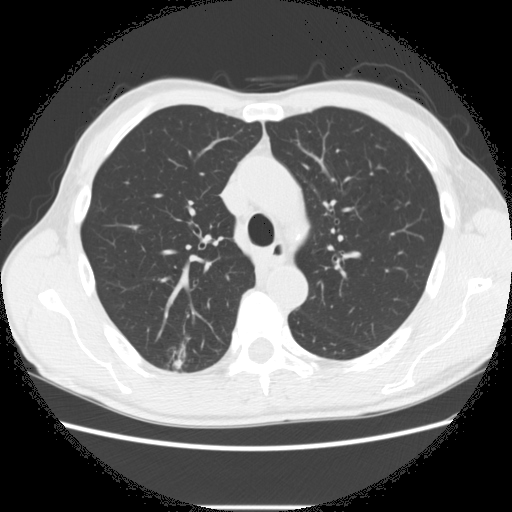
Low-dose screening chest CT, axial slice; second annual screen; lung window (W 1500 / L -600 HU); 2.5 mm slice thickness; standard (soft-tissue) reconstruction kernel (STANDARD); 120 kVp; slice 85 of 282 in the series. Male participant, aged 66 years at enrolment. Former smoker at enrolment.
Lesion marked by an expert reader, bounding box (x1, y1, x2, y2) in pixels: (164, 342, 220, 383). The screening reader recorded 5 non-calcified nodules or masses ≥4 mm on this exam; which of them this box marks is not recorded. Official screen result: positive, change unspecified: nodule(s) >= 4 mm or enlarging nodule(s), mass(es), or other non-specific abnormalities suspicious for lung cancer. Participant outcome: lung cancer diagnosed 75 days after this screen — adenocarcinoma, NOS, right upper lobe, undifferentiated (G4), stage IA (AJCC 6th edition), 20 mm at pathology.